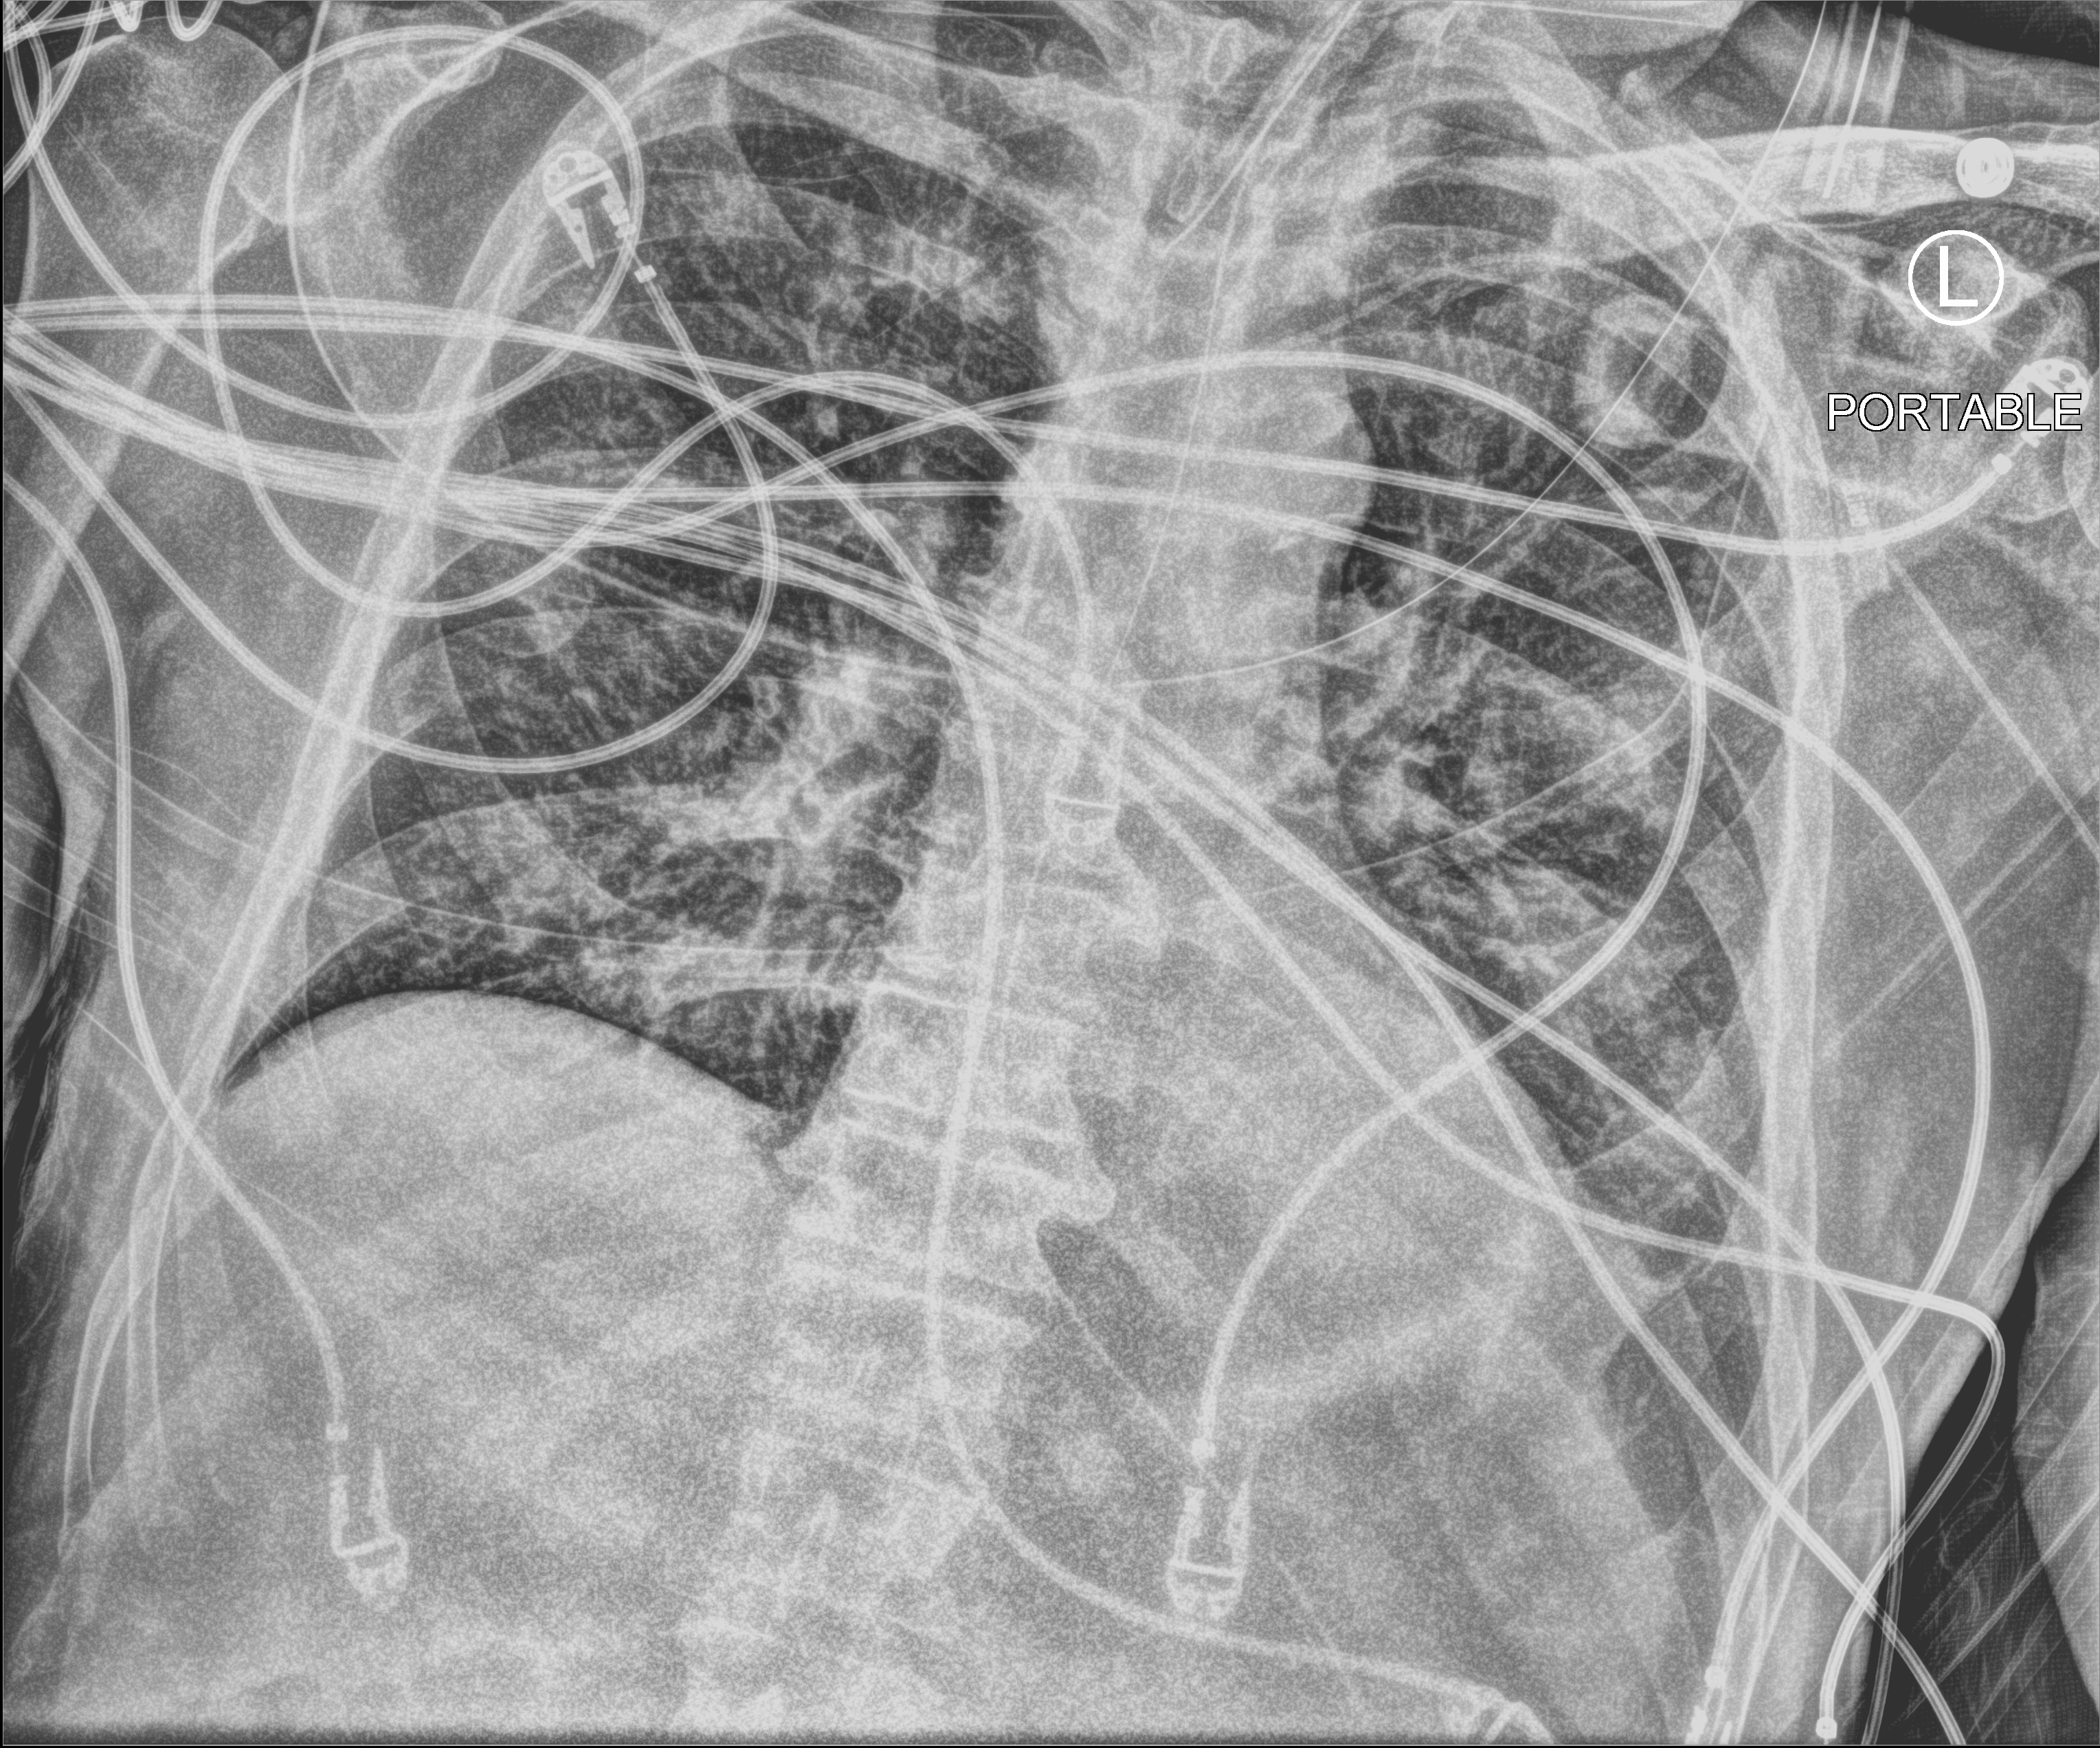
Bedside chest radiograph (computed radiography). Male patient hospitalised with COVID-19, age 60–74 years.
Admission-level facts for this patient (not findings on this image; timing relative to this image not recorded):
- admitted to intensive care during this hospital stay: yes
- mechanically ventilated during this hospital stay: yes
- chronic kidney disease (admission record): no